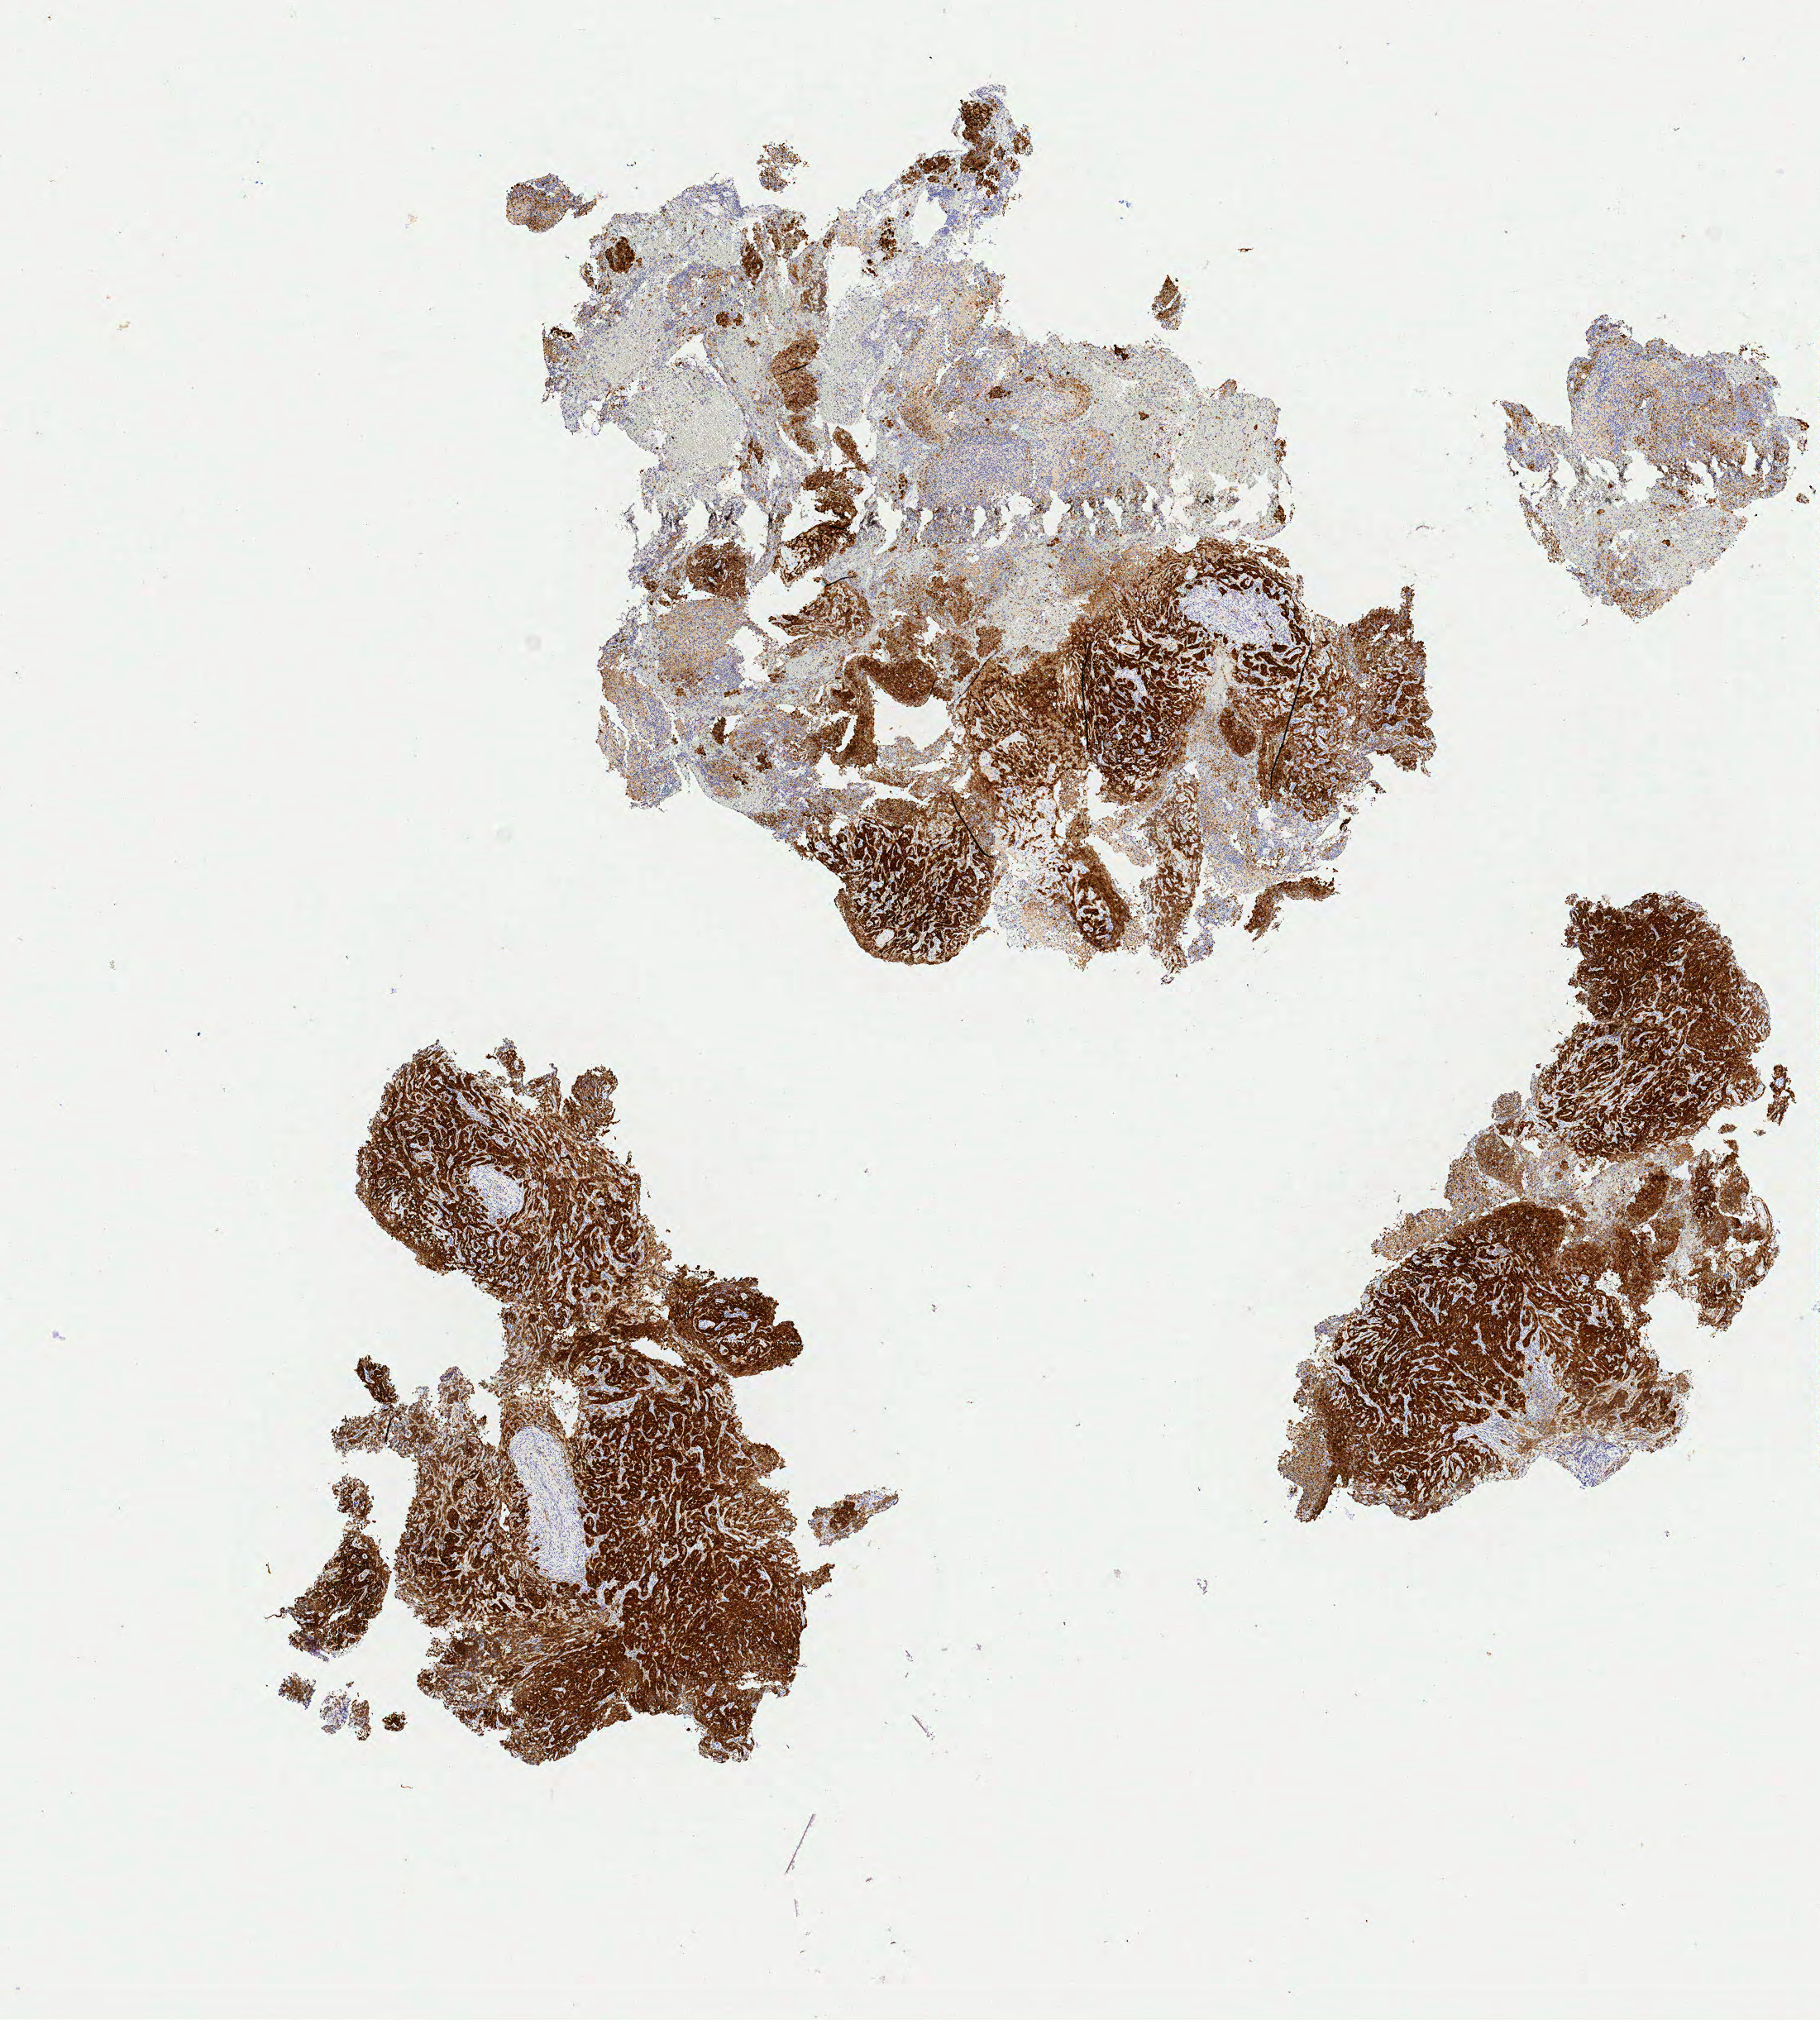
IHC for p16 (p16INK4a), whole-slide image, shown as a low-resolution overview of the whole scanned area (about 8.7 x 9.6 mm); specimen: tumor tissue; site: cervix. Patient: female, 41 years old.
Diagnosis: Squamous cell carcinoma, large cell, nonkeratinizing, NOS.